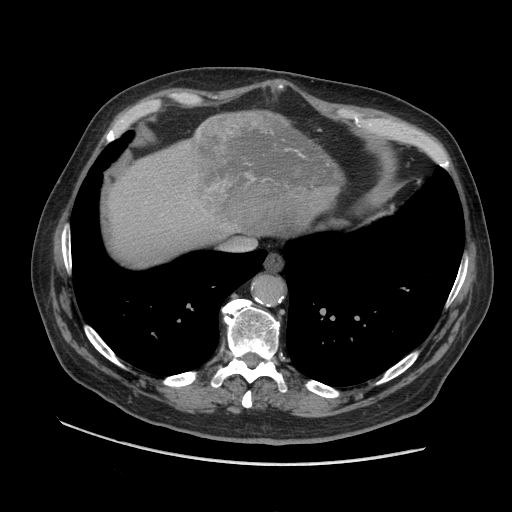
Contrast-enhanced abdominal CT (liver protocol), one axial slice; position 88 of 109 along the scan axis; reconstruction kernel STANDARD; soft-tissue window (W 400 / L 40 HU); 512 × 512 image matrix, field of view 420 × 420 mm. From the clinical record (not read from this slice): diagnosis: hepatocellular carcinoma (patient treated with transarterial chemoembolisation; whether this scan precedes or follows treatment is not stated here); TNM stage (as recorded): Stage-I; Child-Pugh class: A; tumour nodularity: uninodular.
Structures marked on this image (semi-automatically segmented with operator editing):
- liver parenchyma outside the tumour (the mass and vessels are separate outlines, so this box may not span the whole liver): bounding box <108,110,338,264> (left, top, right, bottom; pixels)
- mass: <188,111,344,232>